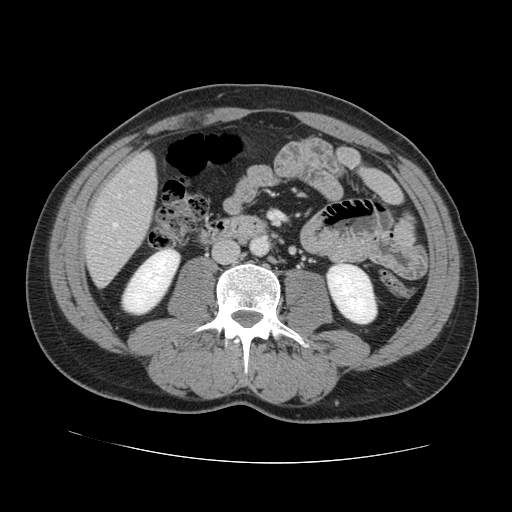
Contrast-enhanced abdominal CT, one axial slice; slice 31 of 131 in the series (ordered by position); 120 kVp; intravenous contrast given; soft-tissue window (W 400 / L 40 HU); 2.5 mm slice thickness; 512 × 512 image matrix, field of view 380 × 380 mm. Male patient, age 40 years. From the clinical record (not read from this slice): diagnosis: colorectal cancer liver metastases, imaged before liver resection; multiple liver metastases: yes.
Annotated regions visible in this slice (outlined manually by an expert reader):
- hepatic veins: box from (x=113, y=195) to (x=120, y=227) px
- liver: (x=86, y=154)–(x=157, y=285)